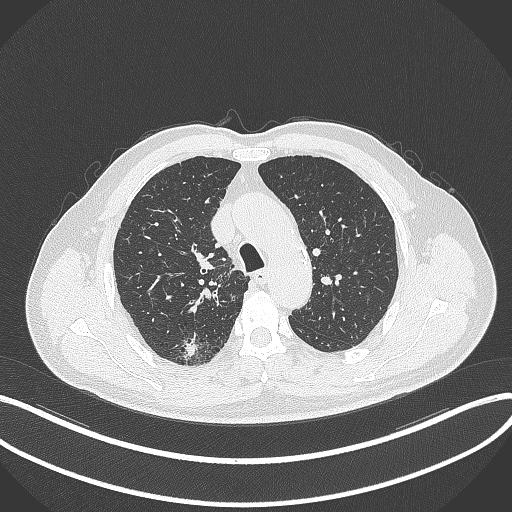
Chest CT, one axial slice. Position 272 of 359 along the scan axis. 120 kVp. Lung window (W 1500 / L -600 HU). 1 mm slice thickness. 512 × 512 image matrix, field of view 400 × 400 mm. Male patient, age 69 years. Case-level facts recorded for this patient, not image findings: clinical TNM (as recorded): T1b N0 M0.
Outlined on this slice (rectangle marked by the reading radiologist):
- lung tumour (recorded histology: adenocarcinoma): bounding box <181,337,199,364> (left, top, right, bottom; pixels)